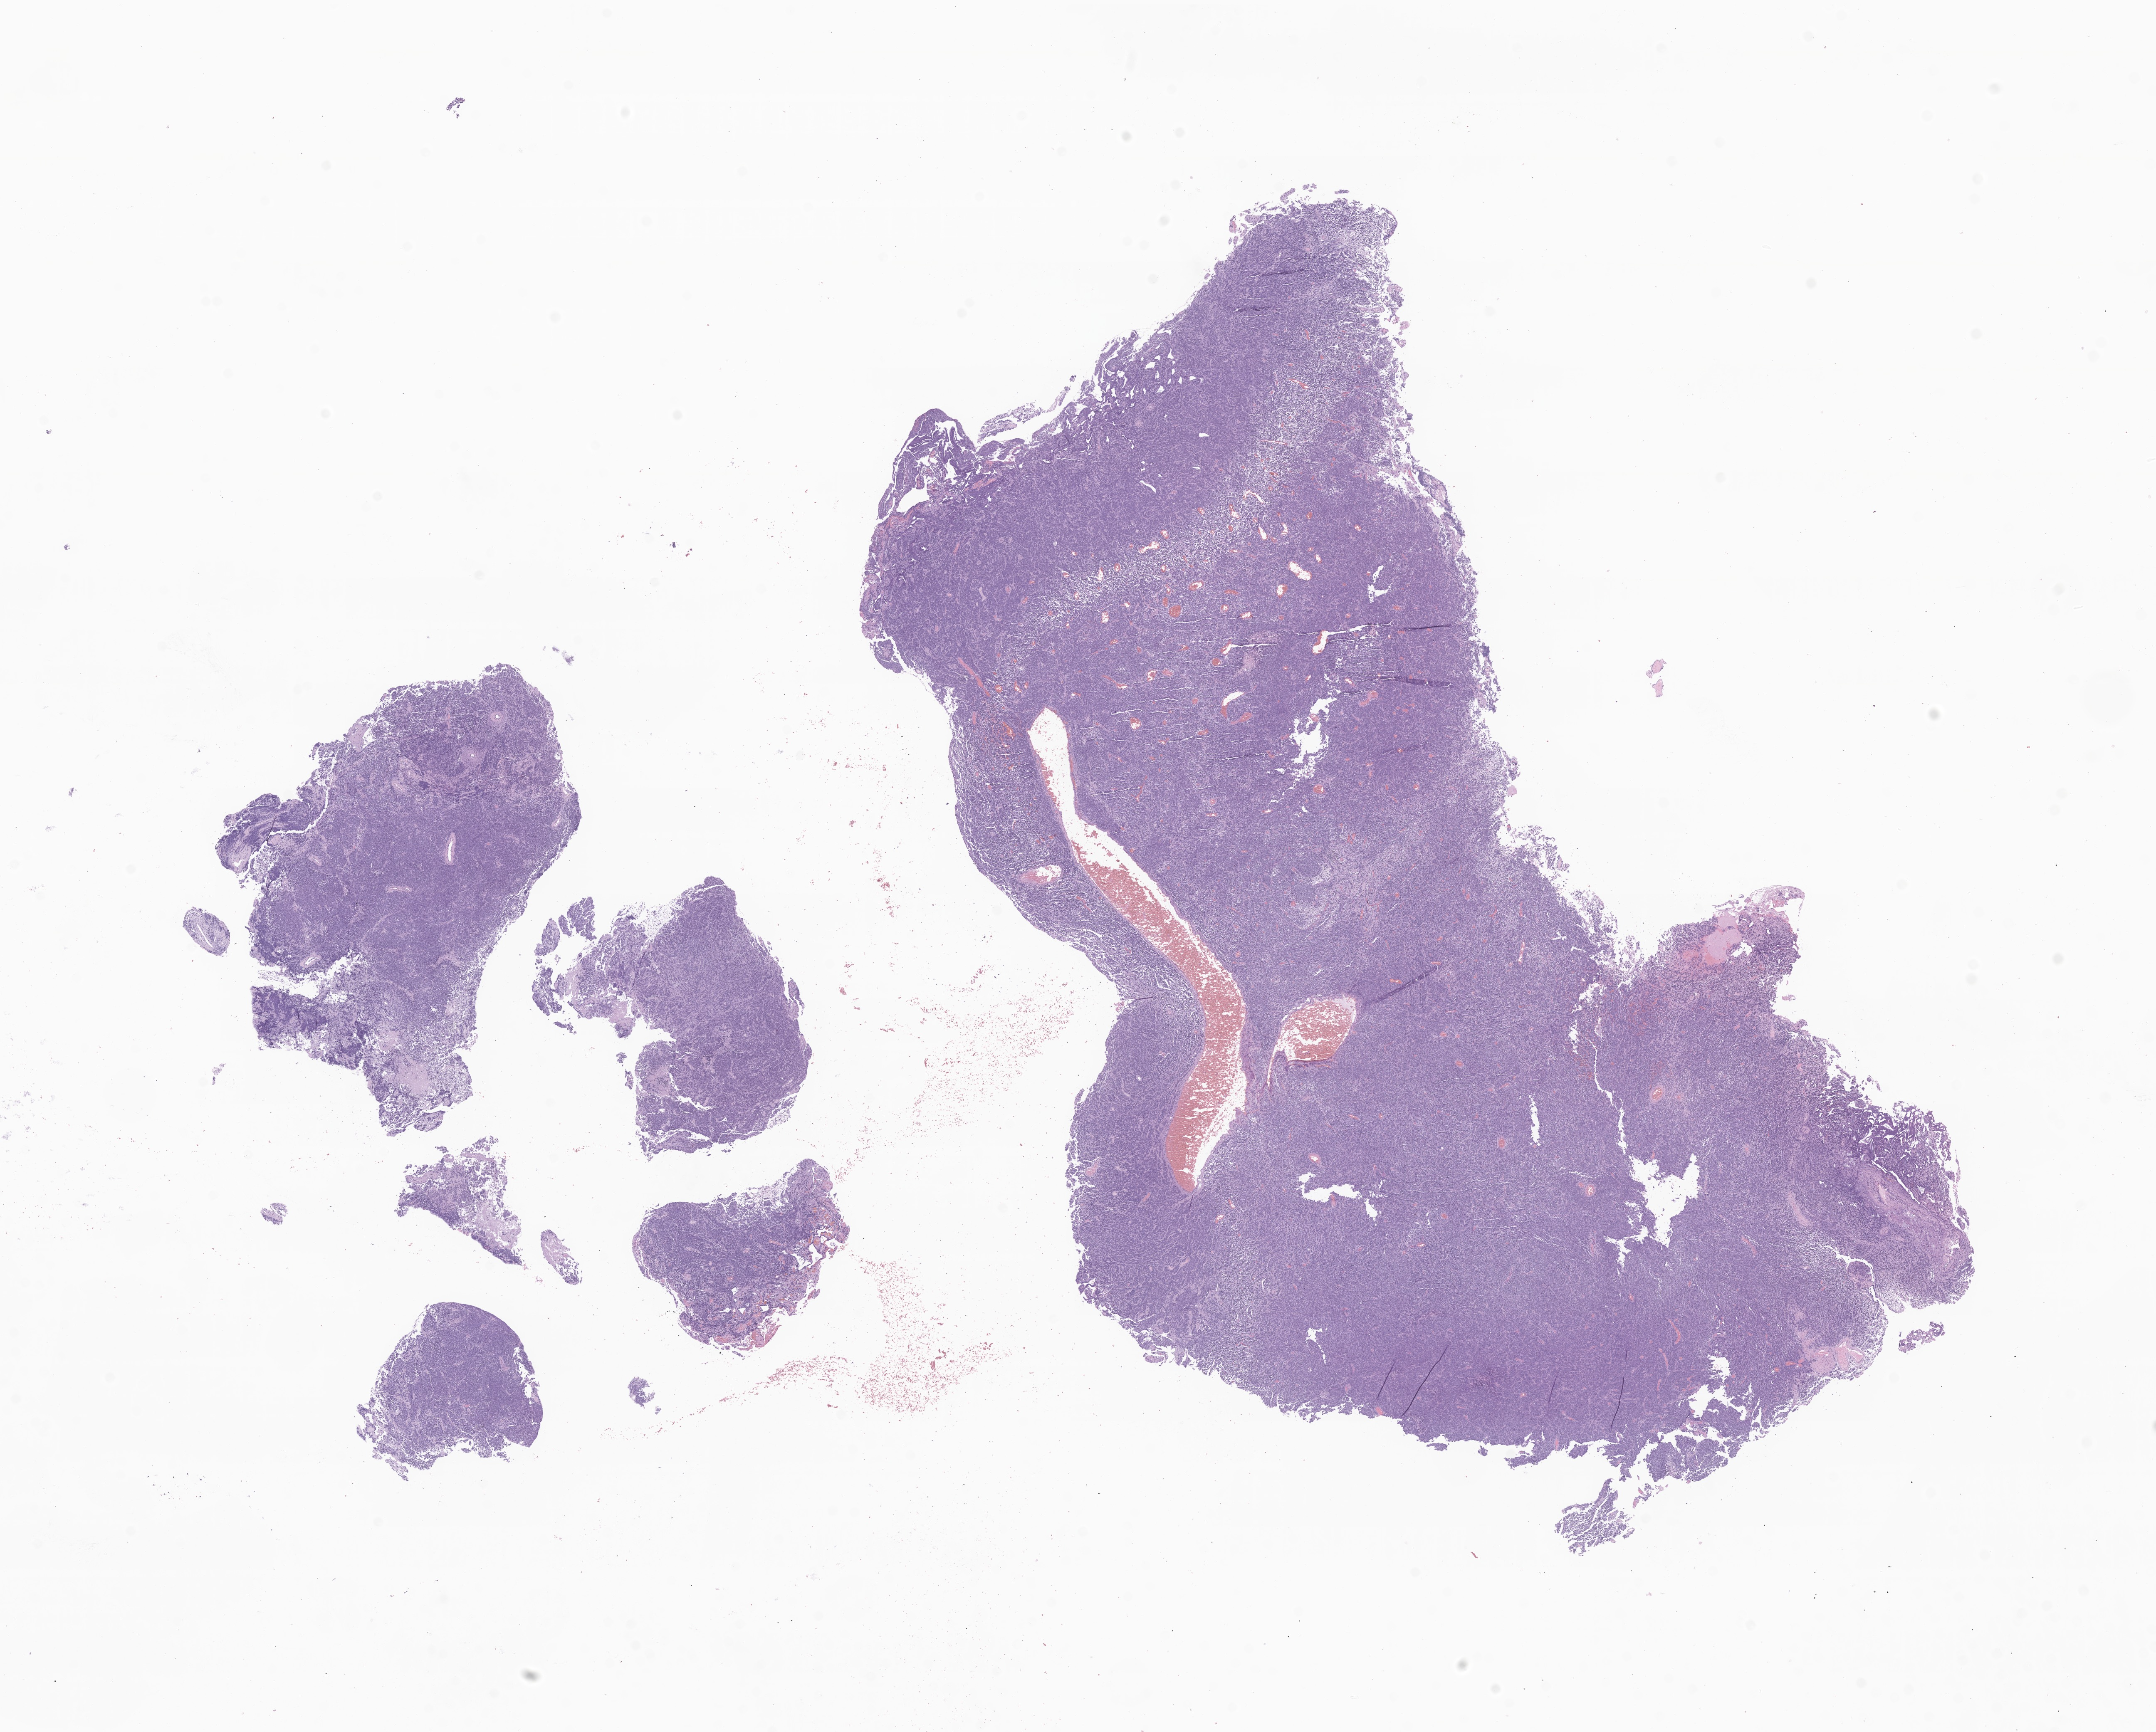
Whole-slide image, hematoxylin and eosin (H&E) stain of tumor tissue from the cerebral ventricle — a low-resolution overview of the entire scanned area, about 21.9 x 17.6 mm; formalin-fixed paraffin-embedded section. Patient male; age 199 months (16 years 7 months).
Diagnosis (ICD-O-3 morphology term): Medulloblastoma, NOS.